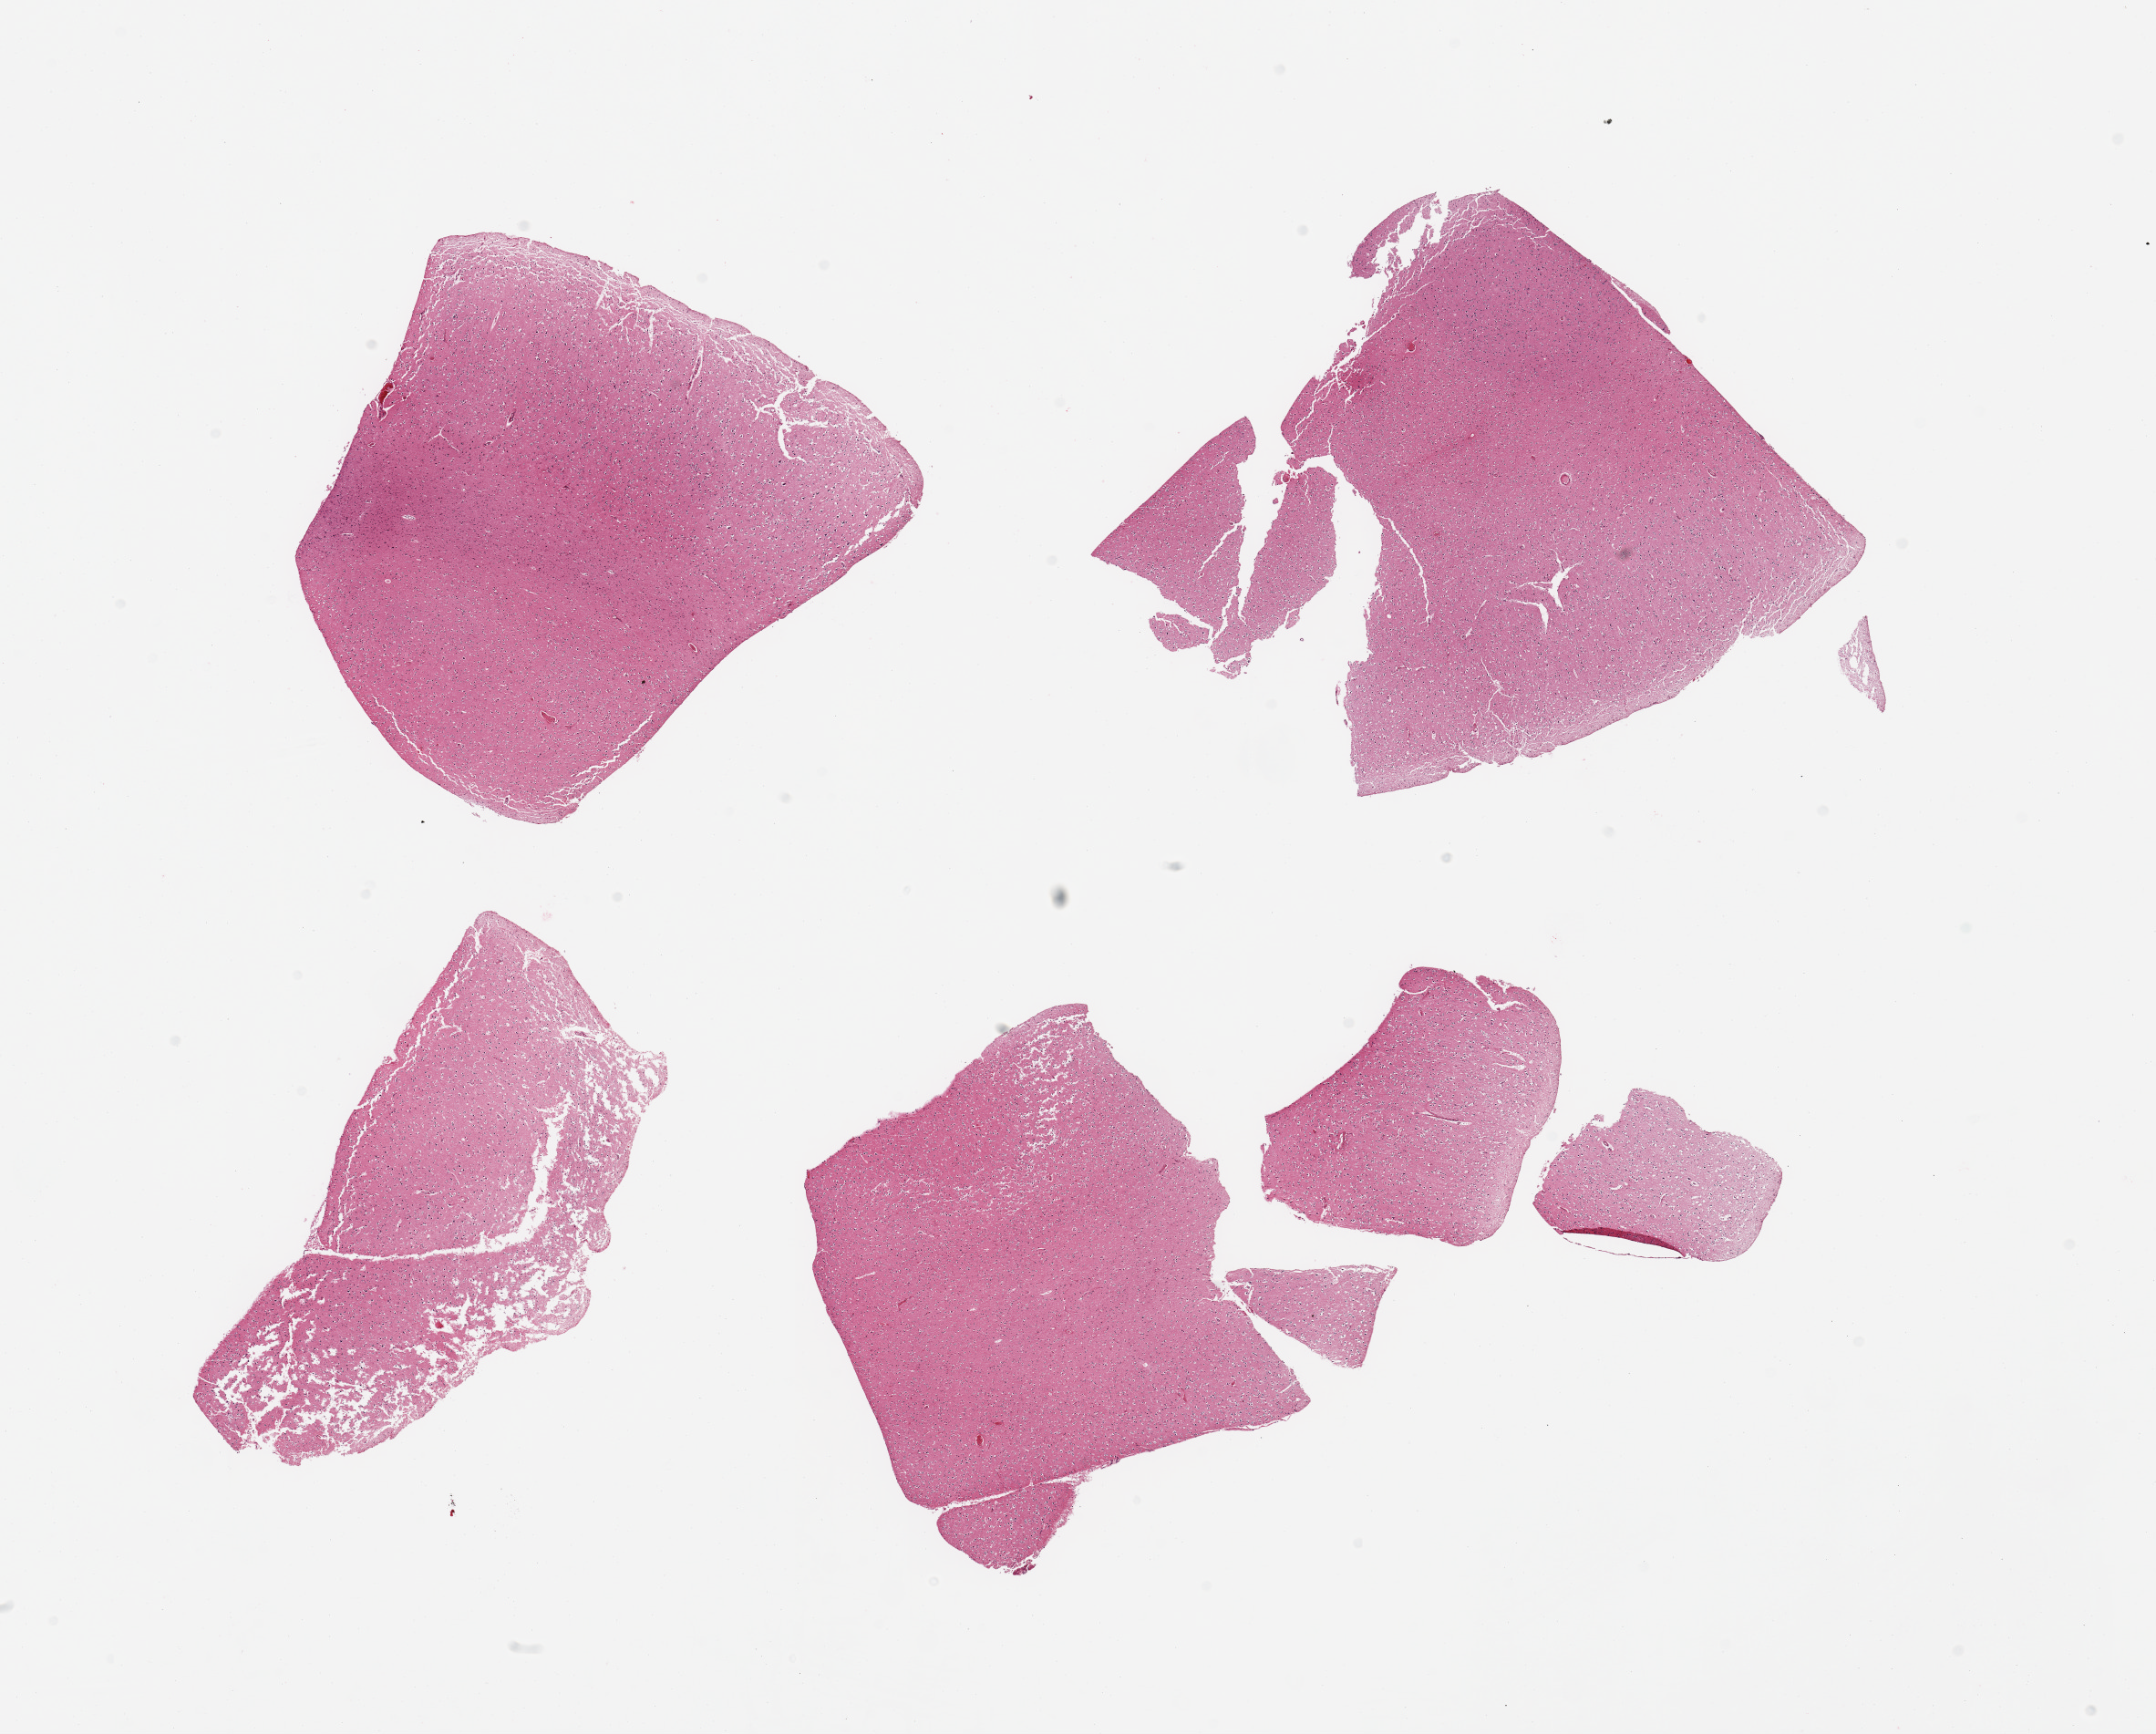
Digitized H&E-stained section — a low-resolution overview of the entire scanned area, about 18.7 x 15.0 mm. PAXgene-fixed, paraffin-embedded tissue. Section of cerebral cortex (target tissue). Tissue donor sample. Donor sex: male.
Review note (as recorded): 4 pieces, no abnormalities.